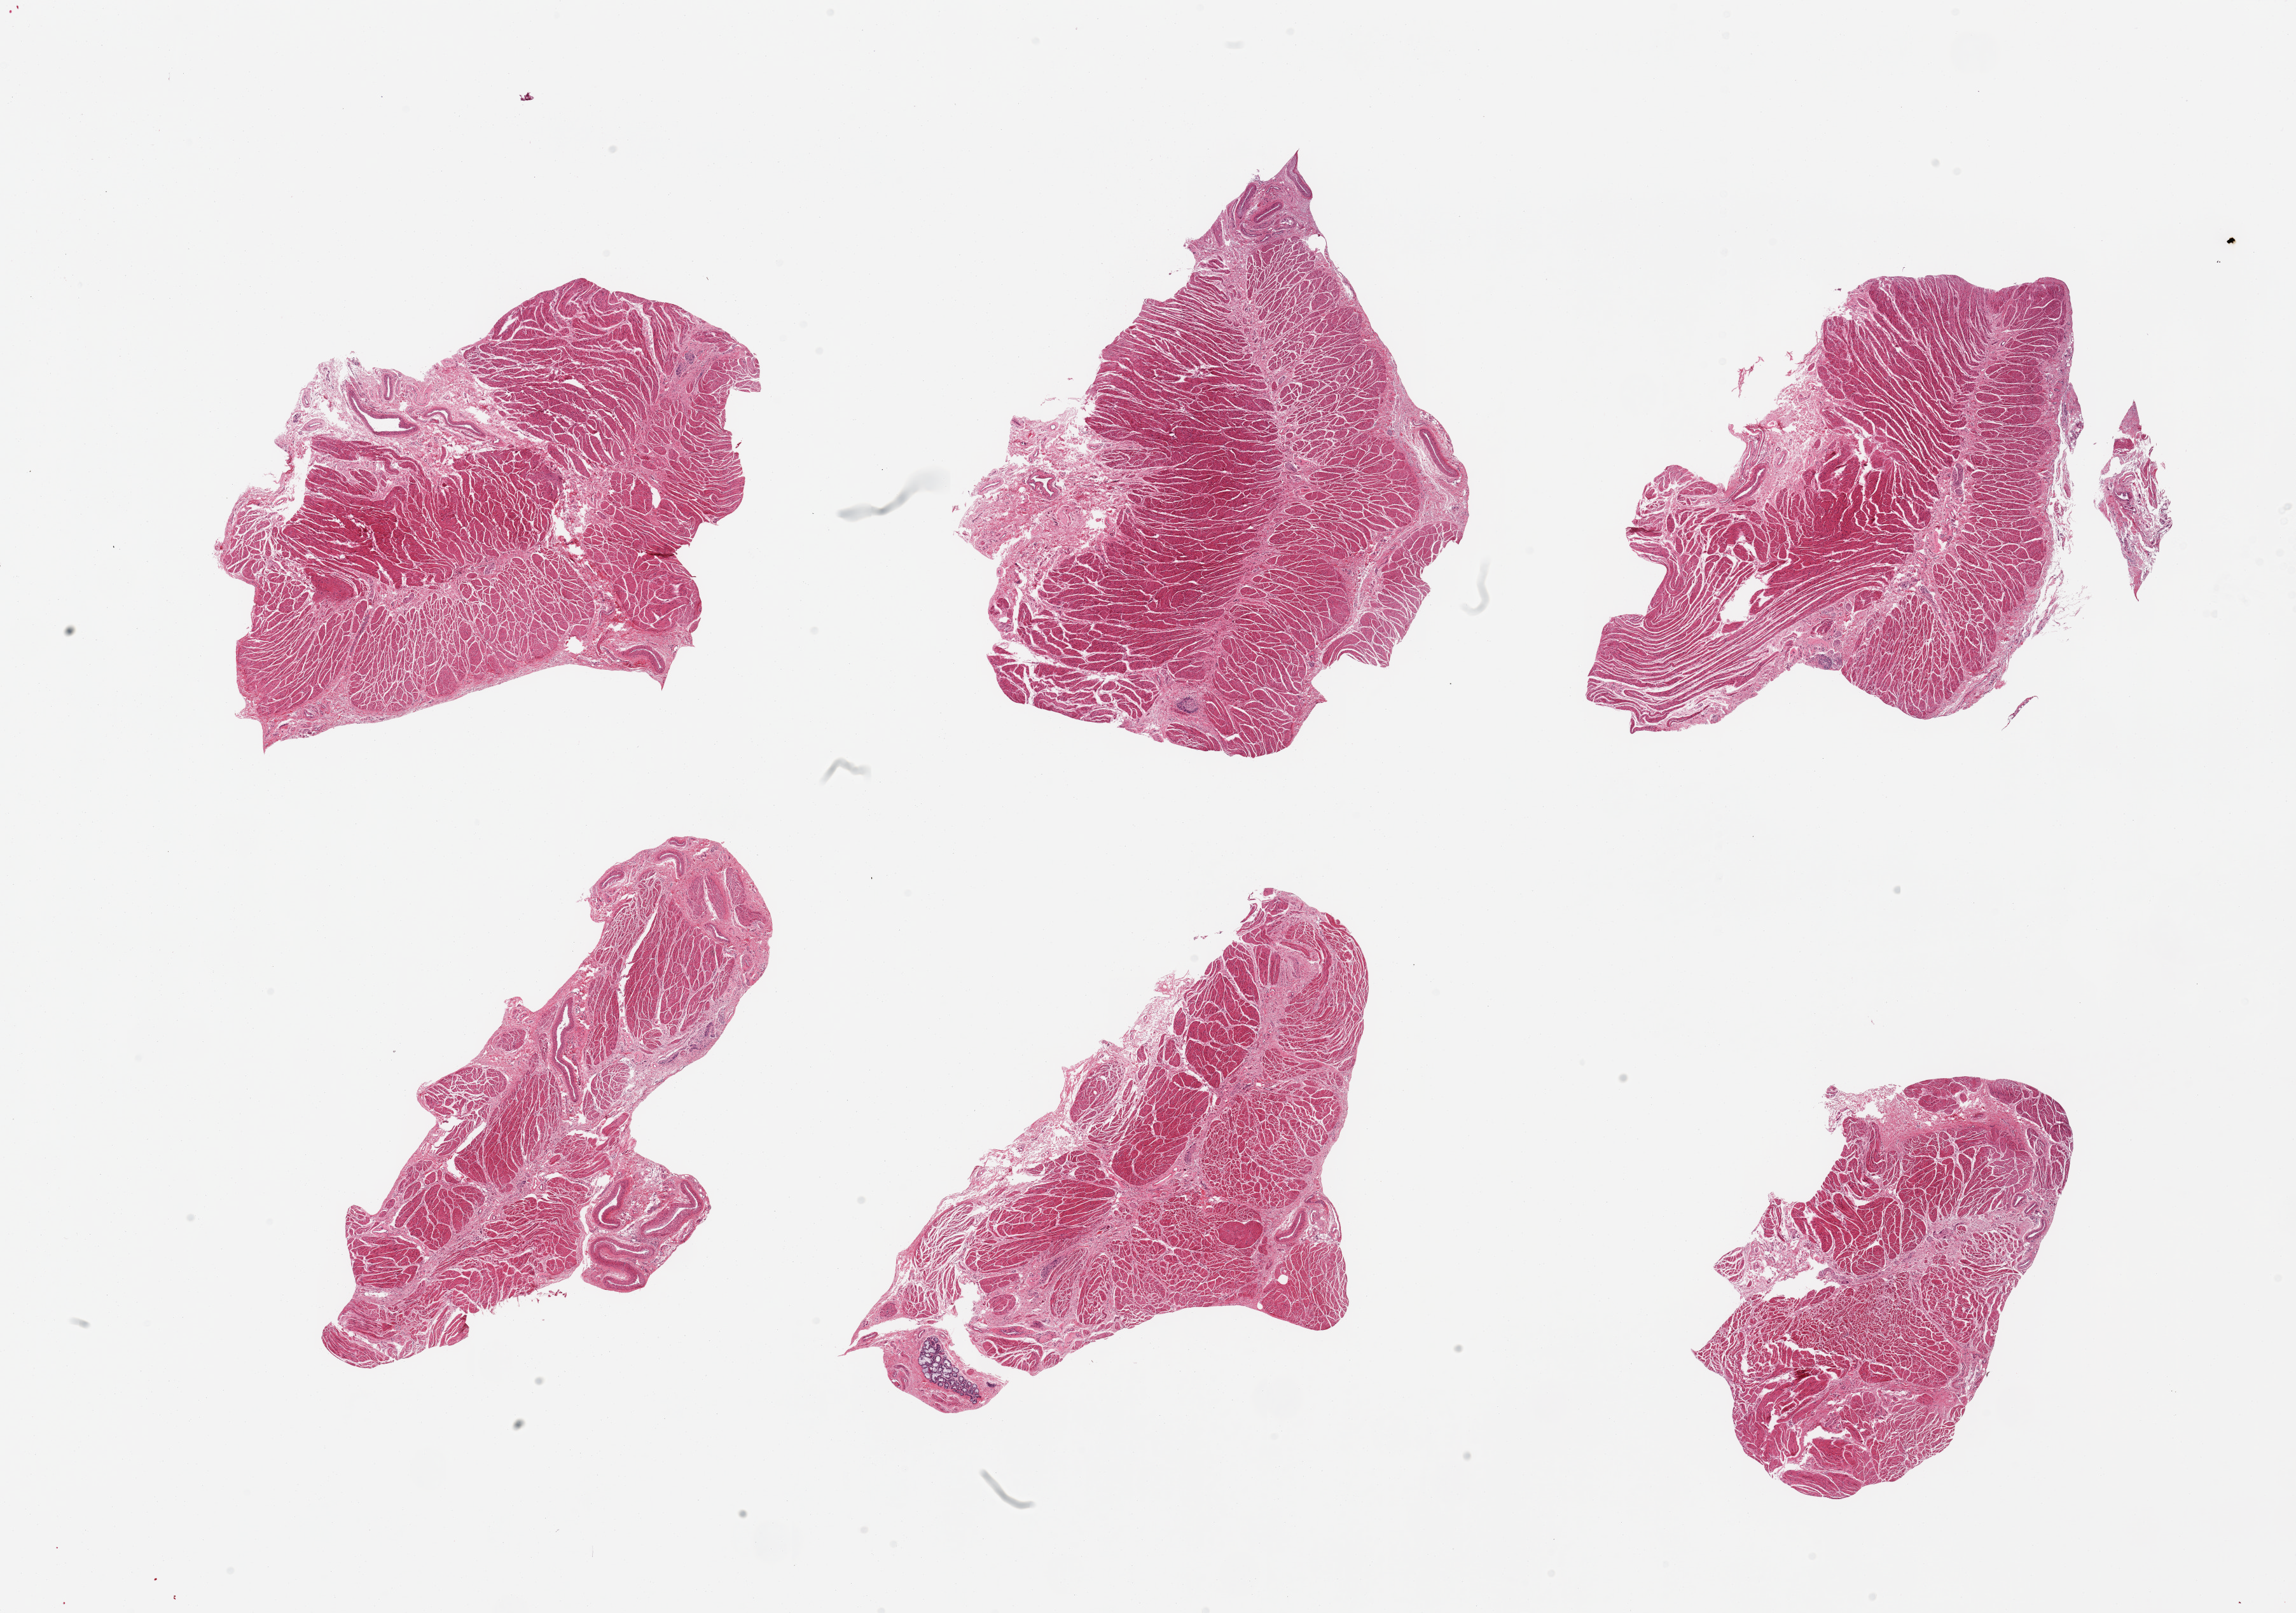
Haematoxylin and eosin whole-slide image, whole scanned area (about 28.5 x 20.1 mm) shown as a low-resolution overview; PAXgene-fixed, paraffin-embedded tissue; sampled site (target tissue): gastroesophageal junction; donor tissue sample. Male donor.
Review note (as recorded): 6 pieces, all target muscularis.